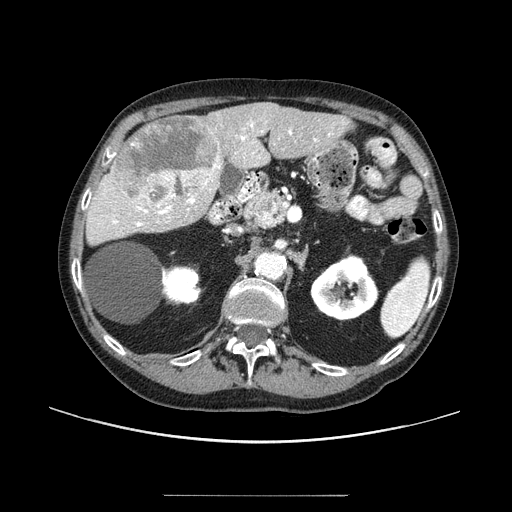
Contrast-enhanced abdominal CT (liver protocol), one axial slice. Position 47 of 91 along the scan axis. One of 2 acquisitions stored at this slice position. Soft-tissue window (W 400 / L 40 HU). 2.5 mm slice thickness. 512 × 512 image matrix, field of view 400 × 400 mm. From the clinical record (not read from this slice): diagnosis: hepatocellular carcinoma (patient treated with transarterial chemoembolisation; whether this scan precedes or follows treatment is not stated here); TNM stage (as recorded): Stage-I; Child-Pugh class: A; tumour differentiation: moderately differentiated.
Structures marked on this image (semi-automatically segmented with operator editing):
- liver parenchyma outside the tumour (the mass and vessels are separate outlines, so this box may not span the whole liver): bounding box [x1, y1, x2, y2] px = [88, 102, 350, 244]
- mass: [113, 115, 220, 211]
- liver vessels: [112, 121, 330, 227]